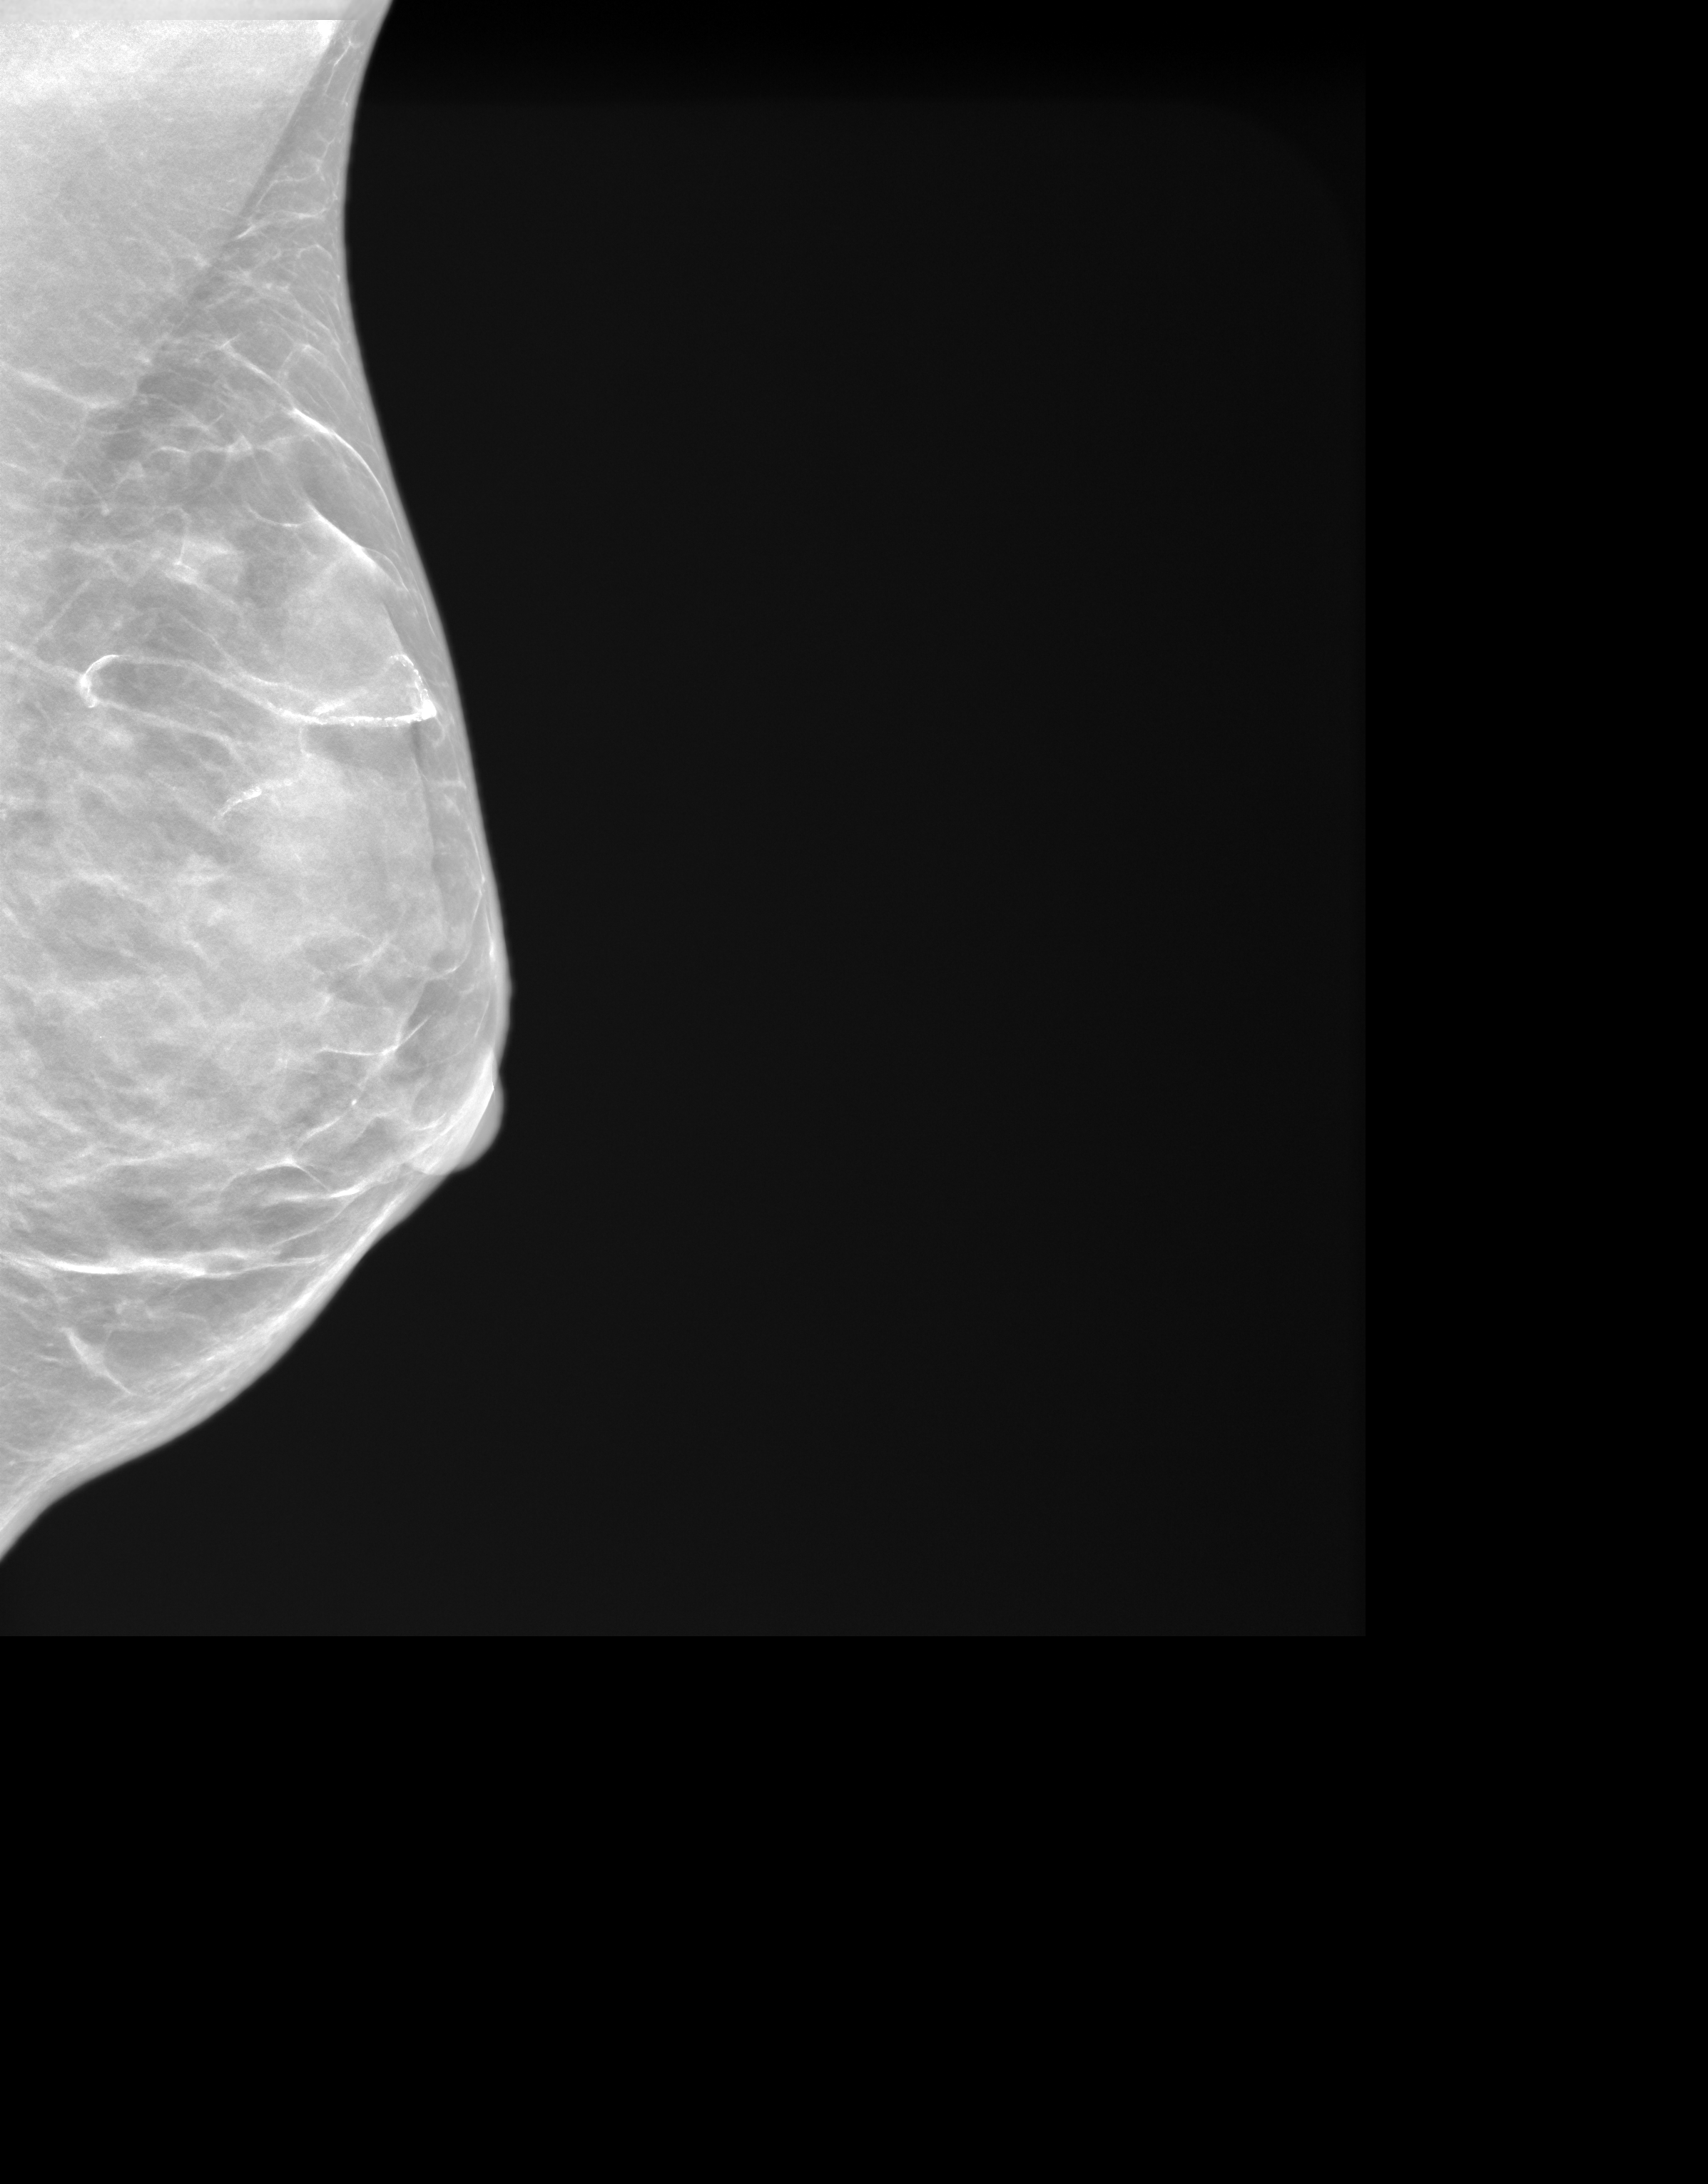
Synthesized 2-D mammogram reconstructed from digital breast tomosynthesis, left breast, MLO view, screening examination, system: SenoIris_1SP1.1(421). Female patient, age 59 years.
Breast density at the screening exam (both breasts): extremely dense (BI-RADS density category d). Final BI-RADS assessment for this screening round (tomosynthesis exam, both breasts): category 1. Recall: no recall after this screen.